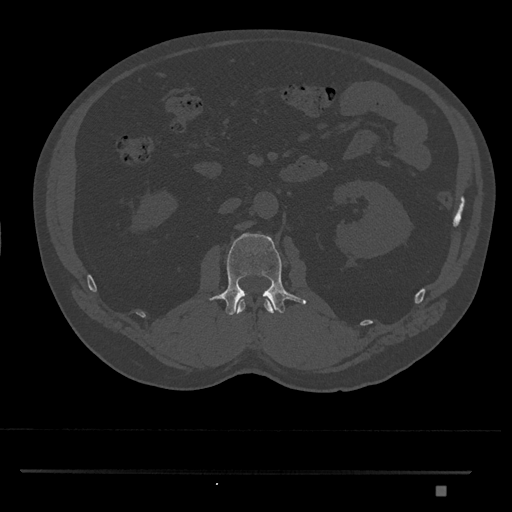
CT including the spine, one axial slice. Slice 768 of 1134 in the series (ordered by position). Bone window (W 1800 / L 400 HU). 512 × 512 image matrix, field of view 429 × 429 mm. Male patient, age 65 years. From the clinical record (not read from this slice): primary cancer: prostate.
Outlined on this slice (semi-automatic segmentation, software-assisted and operator-edited):
- L1 vertebra: bounding box (x1, y1, x2, y2) in pixels: (235, 298, 275, 315)
- L2 vertebra: (209, 233, 307, 315)